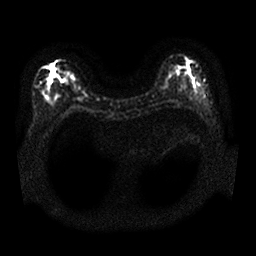
Breast MRI, one axial slice. Slice 9 of 25 in the series (ordered by position). Diffusion-weighted series; image 2 of 4 stored at this slice position (different b-values; order by instance number). 1.5 T. 4 mm slice thickness. 256 × 256 image matrix, field of view 340 × 340 mm. Female patient.
Outlined on this slice (manually delineated by an expert):
- tumour on diffusion-weighted imaging: bounding box <45,64,54,83> (left, top, right, bottom; pixels)